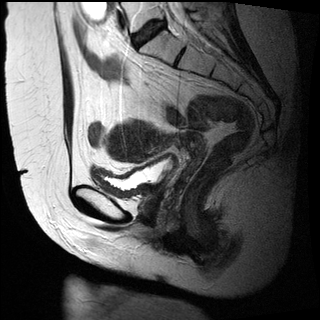
Pelvic MRI for cervical cancer, one sagittal slice; position 13 of 27 along the scan axis; T2-weighted; 1.5 T; TE 89 ms, TR 2740 ms; 4 mm slice thickness; 320 × 320 image matrix, field of view 260 × 260 mm. Female patient, age 47 years.
Annotated regions visible in this slice (manually delineated by an expert):
- uterus and cervix: box from (x=106, y=119) to (x=197, y=164) px